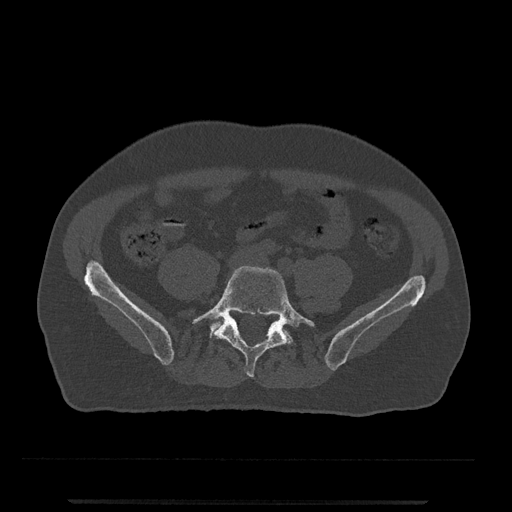
CT including the spine, one axial slice. Slice 71 of 797 in the series (ordered by position). Reconstruction kernel Br40s/3. 120 kVp. Bone window (W 1800 / L 400 HU). 512 × 512 image matrix. Patient: male, 63 years. From the clinical record (not read from this slice): primary cancer: prostate.
Structures marked on this image (semi-automatically segmented with operator editing):
- L5 vertebra: bounding box (x1, y1, x2, y2) in pixels: (192, 266, 316, 377)